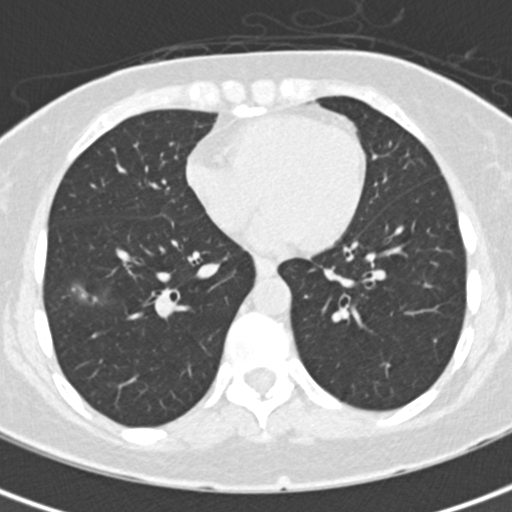
Low-dose screening chest CT, one axial slice. Position 69 of 171 along the scan axis. Lung window (W 1500 / L -600 HU). 2 mm slice thickness. 512 × 512 image matrix.
Structures marked on this image (manually delineated by an expert):
- lesion 1 (tumor, lower lobe of right lung): box from (x=72, y=282) to (x=101, y=305) px